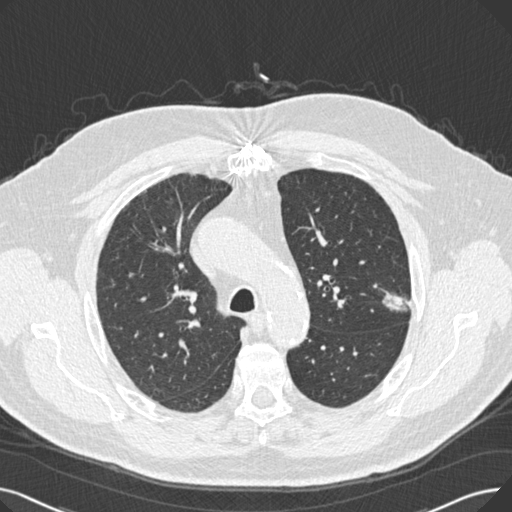
Low-dose screening chest CT, one axial slice. Slice 188 of 269 in the series (ordered by position). Reconstruction kernel B30f. 120 kVp. Lung window (W 1500 / L -600 HU). 1 mm slice thickness. 512 × 512 image matrix, field of view 370 × 370 mm.
Annotated regions visible in this slice (expert manual segmentation):
- lesion 1 (tumor, upper lobe of left lung): bounding box <382,292,411,311> (left, top, right, bottom; pixels)